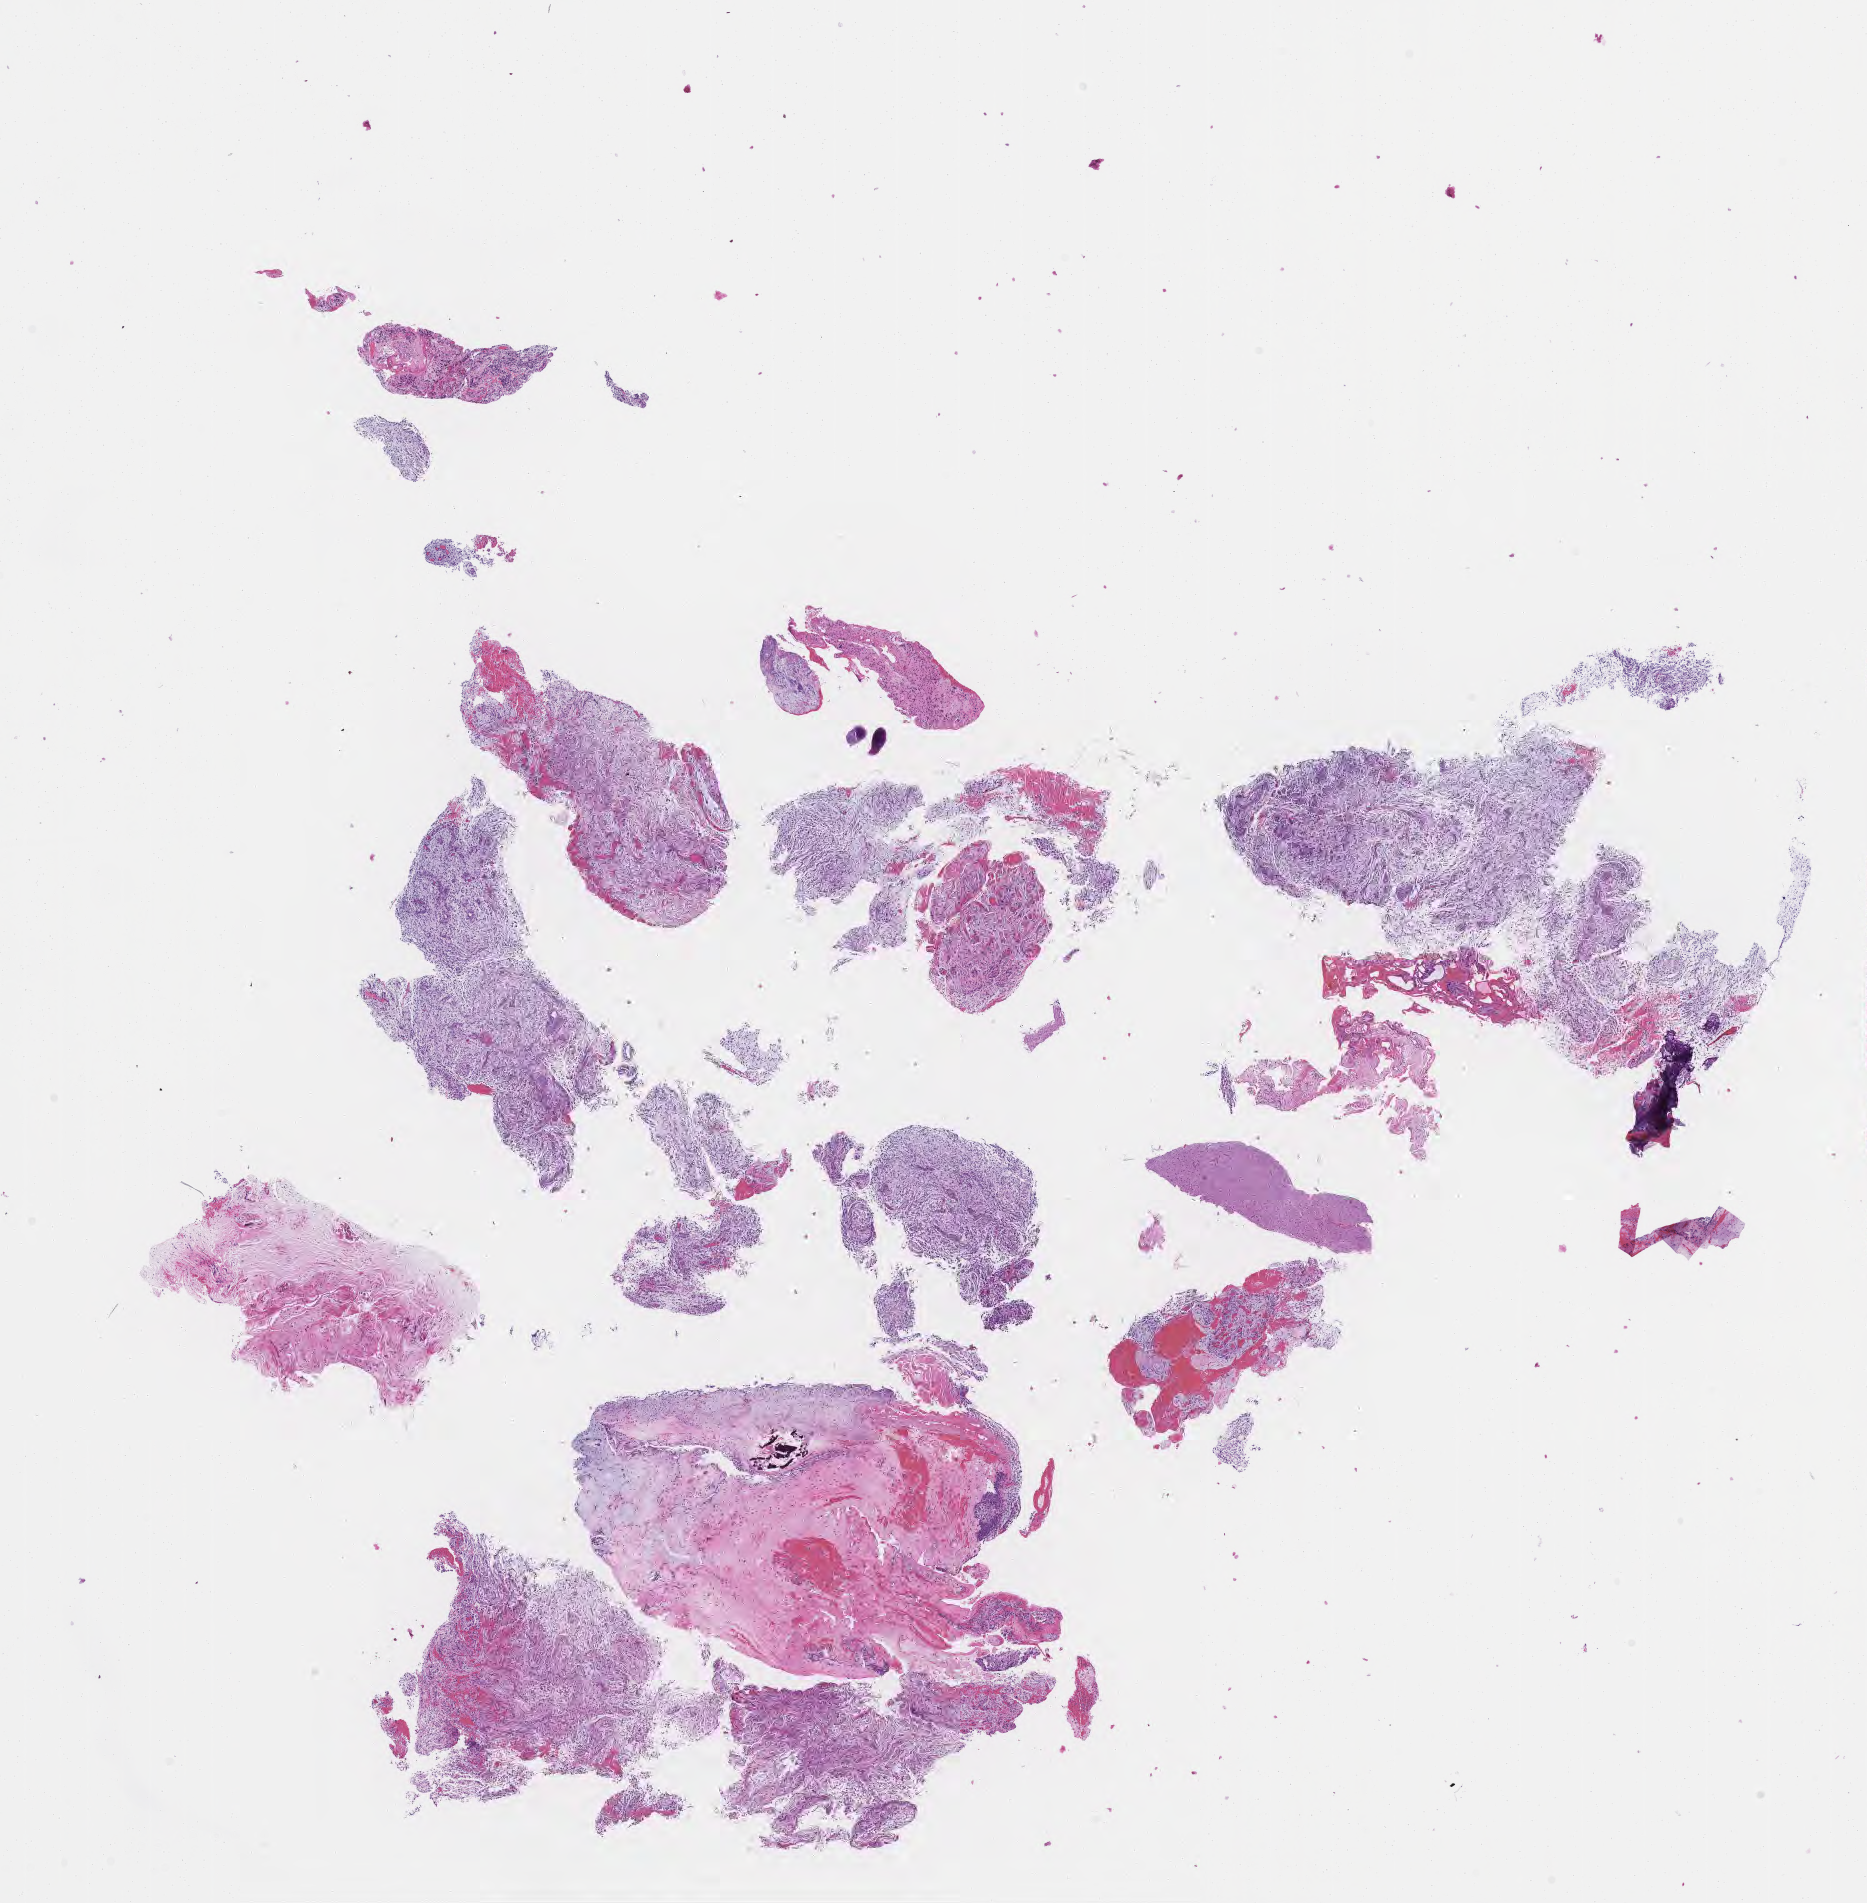
Whole-slide image, haematoxylin and eosin stain of tumor tissue from the brain — low-resolution overview of the scanned area, about 15.1 x 15.4 mm, FFPE section. Patient: male, age 38 months.
• recorded diagnosis: Pilocytic astrocytoma